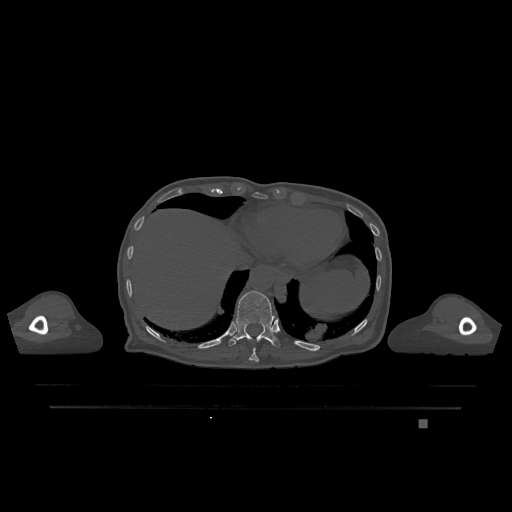
CT including the spine, one axial slice; slice 603 of 1317 in the series (ordered by position); bone window (W 1800 / L 400 HU); 0.5 mm slice thickness; 512 × 512 image matrix. Female patient, age 74 years. Case-level facts recorded for this patient, not image findings: primary cancer: lung.
Outlined on this slice (semi-automatic segmentation, software-assisted and operator-edited):
- T10 vertebra: bounding box [x1, y1, x2, y2] px = [249, 348, 259, 362]
- T11 vertebra: [228, 290, 280, 347]